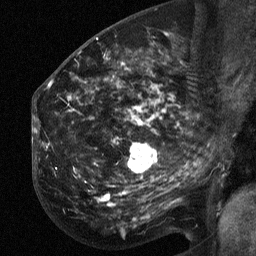
Breast MRI (dynamic contrast-enhanced), one sagittal slice; position 32 of 64 along the scan axis; dynamic contrast-enhanced study with each time point stored as its own series, time point 2 of 3 at this slice position (early post-contrast, ordered by acquisition time); 1.5 T; TE 4.8 ms, TR 27 ms; 256 × 256 image matrix, field of view 200 × 200 mm. Female patient, age 50 years. From the clinical record (not read from this slice): setting: breast cancer imaged before/during neoadjuvant chemotherapy; receptor status: HER2-positive.
Annotated regions visible in this slice (semi-automatic segmentation, software-assisted and operator-edited):
- analysis volume of interest (the breast-tissue region the enhancement analysis was run in; not a lesion): bounding box <53,64,211,212> (left, top, right, bottom; pixels)
- tumour enhancement mask (voxels above the 90 % enhancement threshold inside the analysis volume of interest): <130,144,156,171>